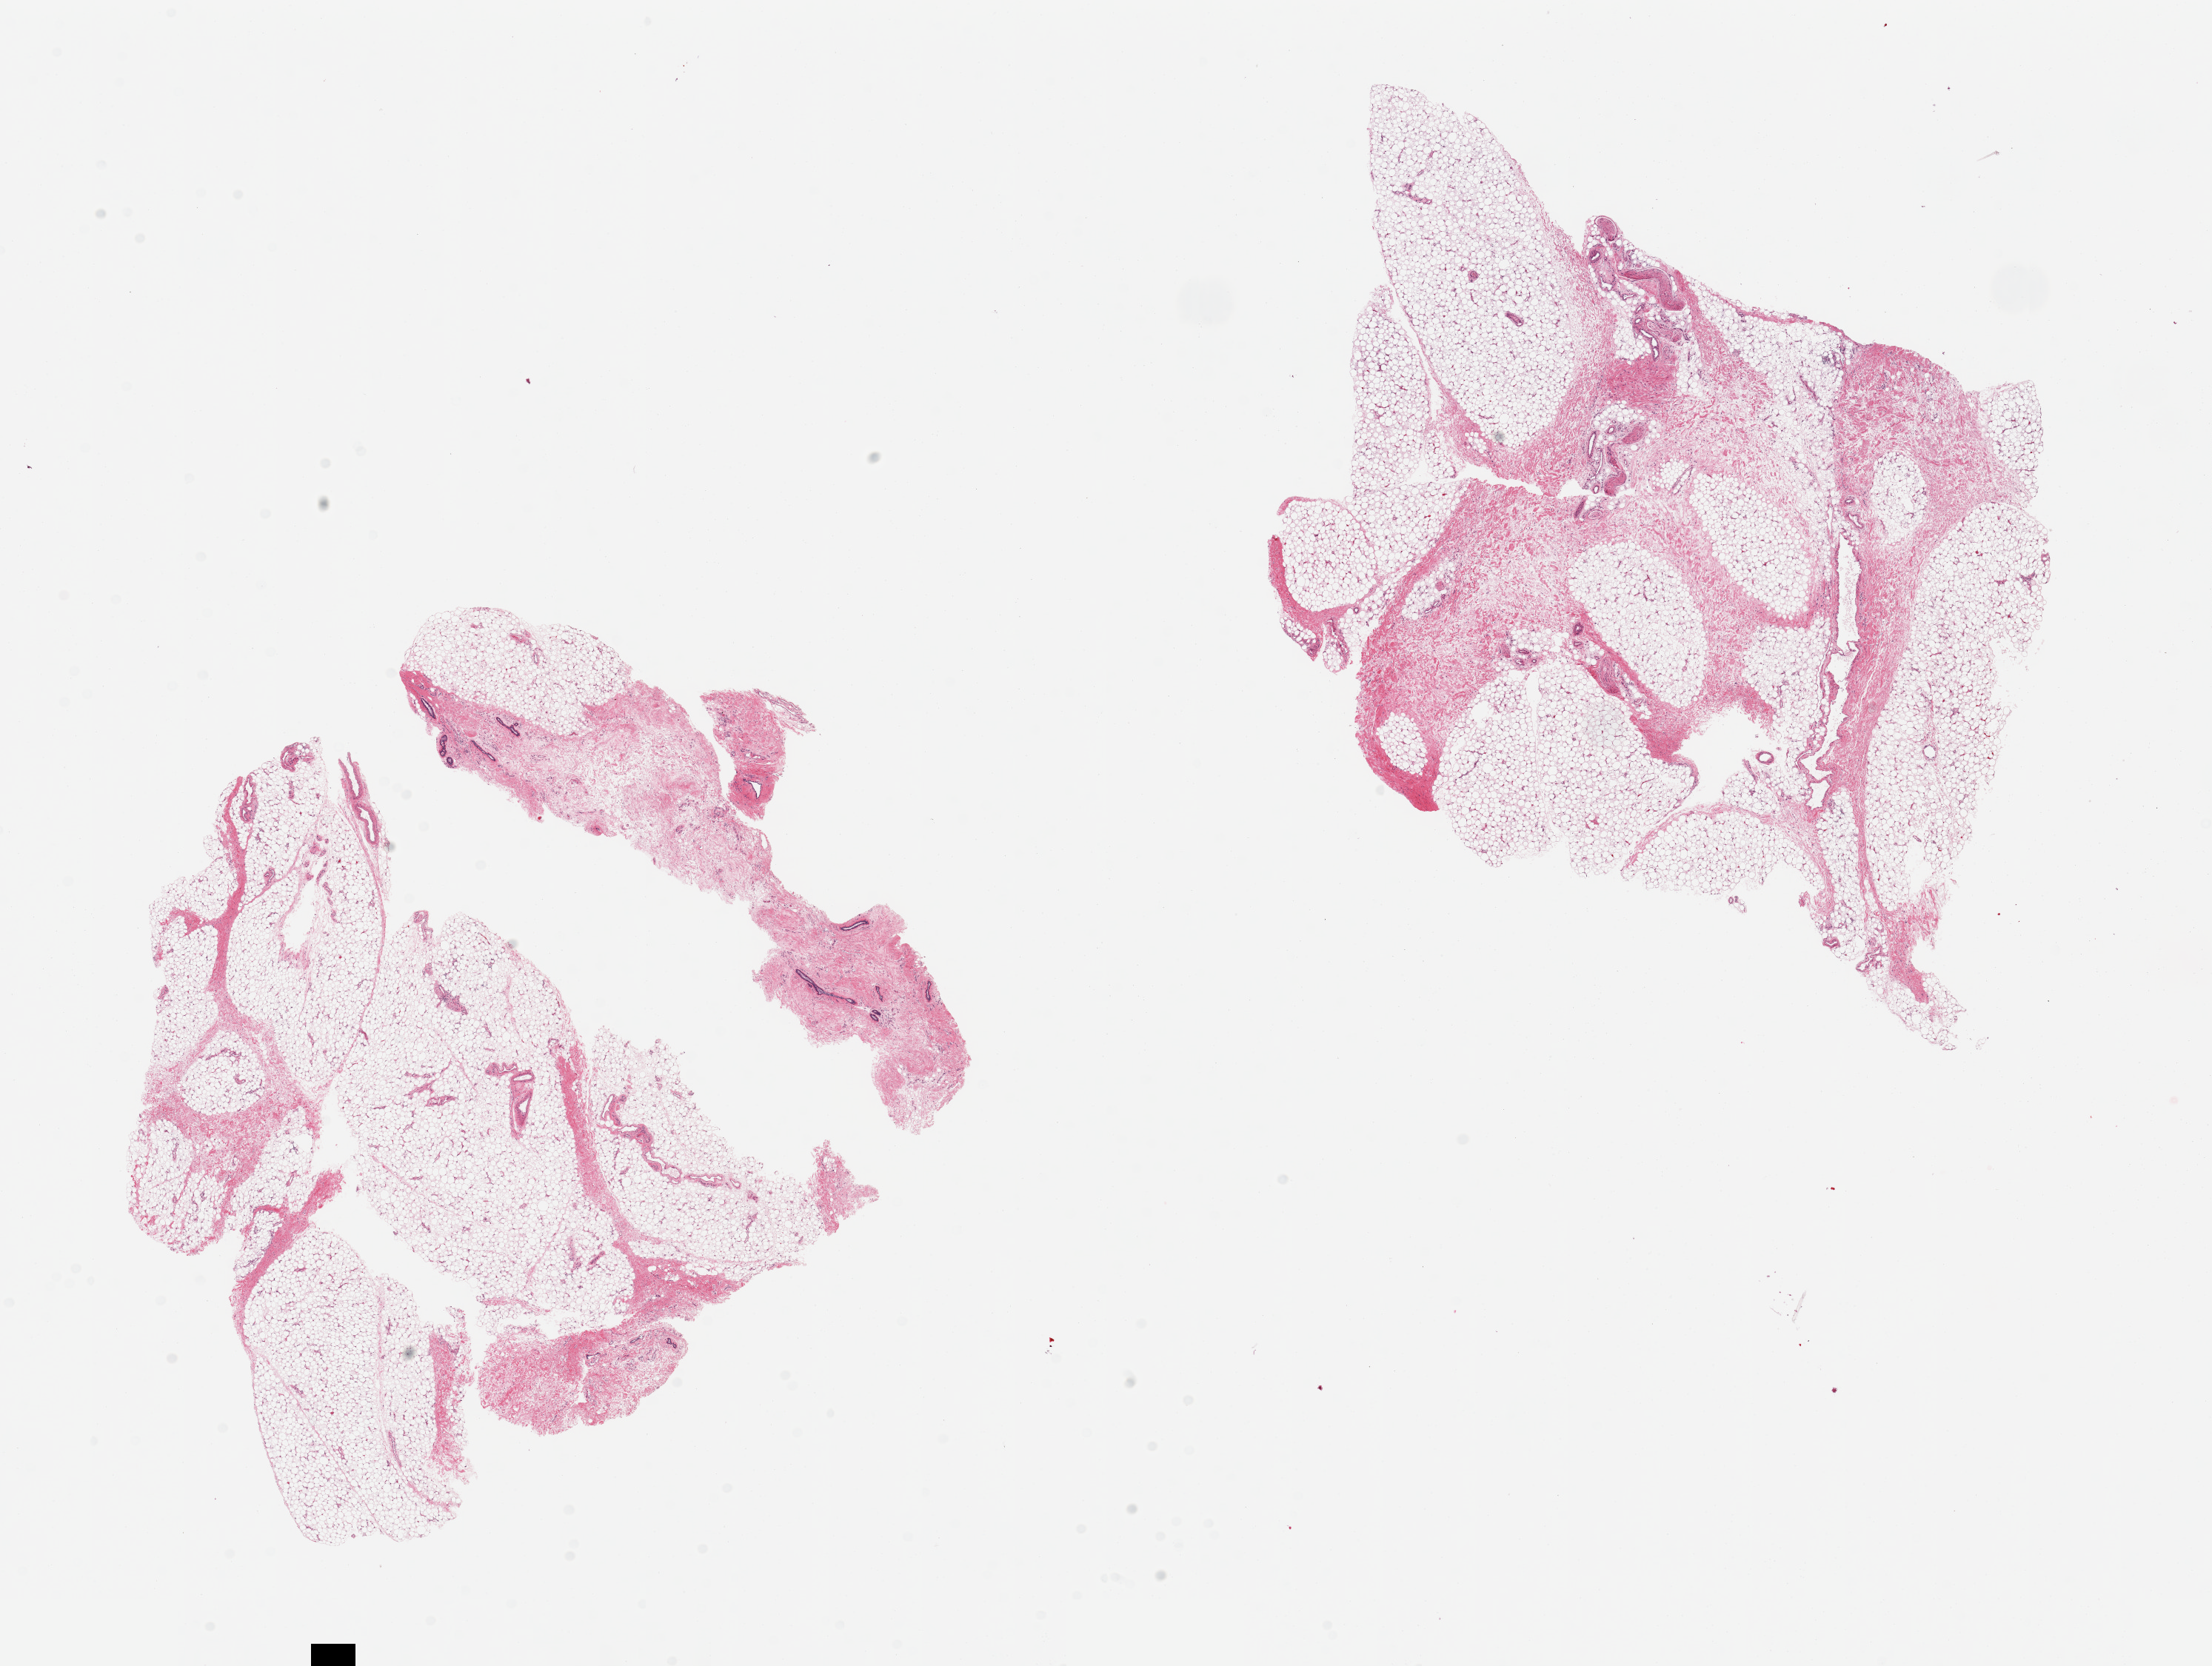
Digitized H&E-stained section — whole scanned area (about 23.6 x 17.8 mm) shown as a low-resolution overview. PAXgene-fixed, paraffin-embedded tissue. Sampled site (target tissue): breast. Donor tissue sample. Male donor.
Pathologist's review note for this sample: 2 pieces; 2 foci of ducts in fibrous stroma.